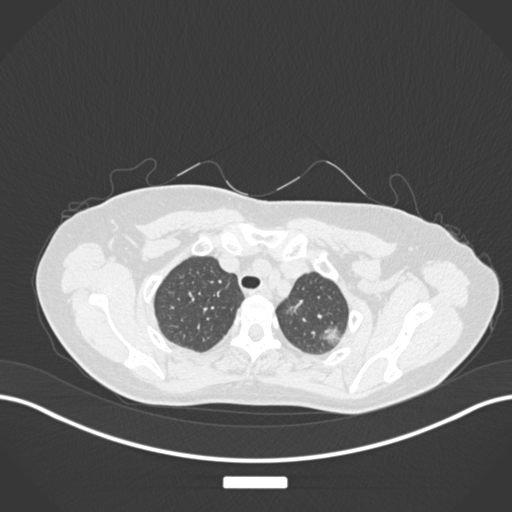
Chest CT, one axial slice. Slice 145 of 181 in the series (ordered by position). Reconstruction kernel B30f. Lung window (W 1500 / L -600 HU). 512 × 512 image matrix, field of view 400 × 400 mm. Patient: female, 58 years. Case-level facts recorded for this patient, not image findings: clinical TNM (as recorded): T1c N0 M0.
Annotated regions visible in this slice (bounding box drawn by a radiologist):
- lung tumour (recorded histology: adenocarcinoma): bounding box <321,322,345,350> (left, top, right, bottom; pixels)